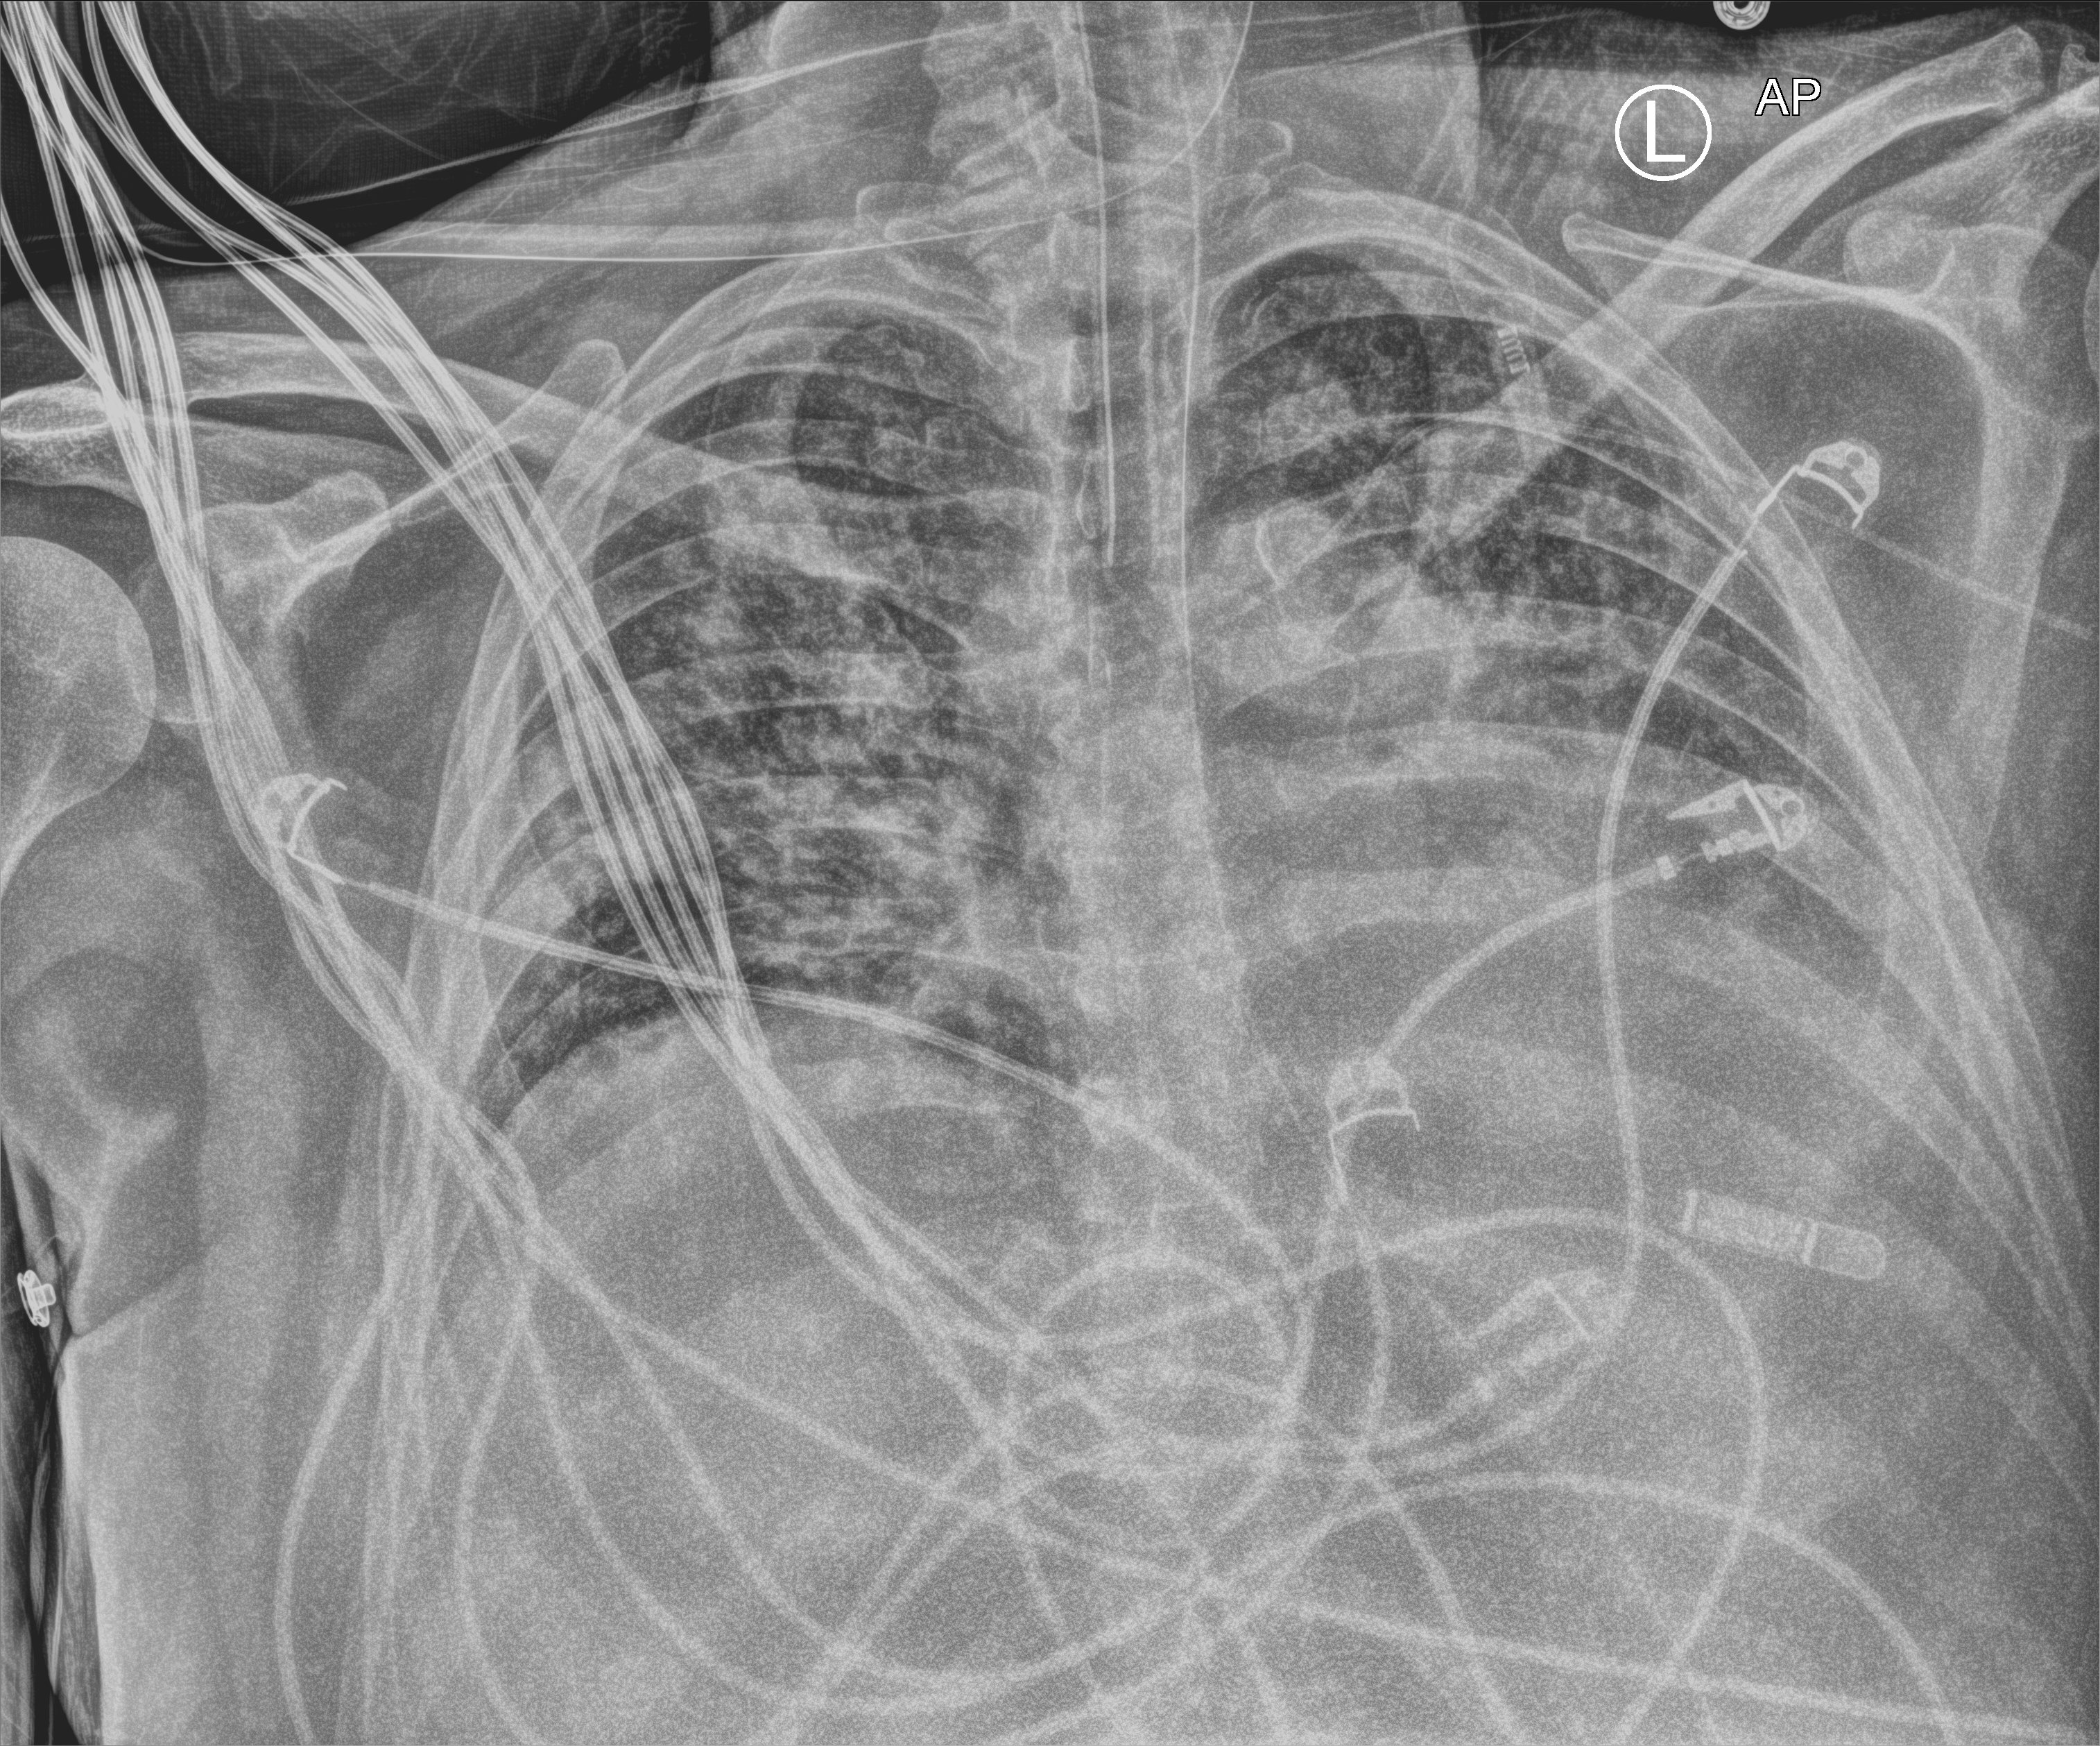
Portable chest radiograph, anteroposterior (AP) projection. Patient hospitalised with COVID-19; male, aged 18–59 years.
Hospital-stay facts (about this admission, not read from this image; timing relative to this image not recorded):
- mechanically ventilated during this hospital stay: yes